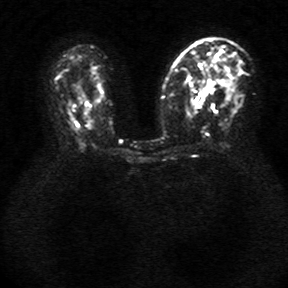
Breast MRI, one axial slice. Position 18 of 34 along the scan axis. Diffusion-weighted series; image 2 of 4 stored at this slice position (different b-values; order by instance number). 1.5 T. 288 × 288 image matrix, field of view 340 × 340 mm. Female patient.
Annotated regions visible in this slice (manually delineated by an expert):
- tumour on diffusion-weighted imaging: box from (x=204, y=80) to (x=211, y=92) px